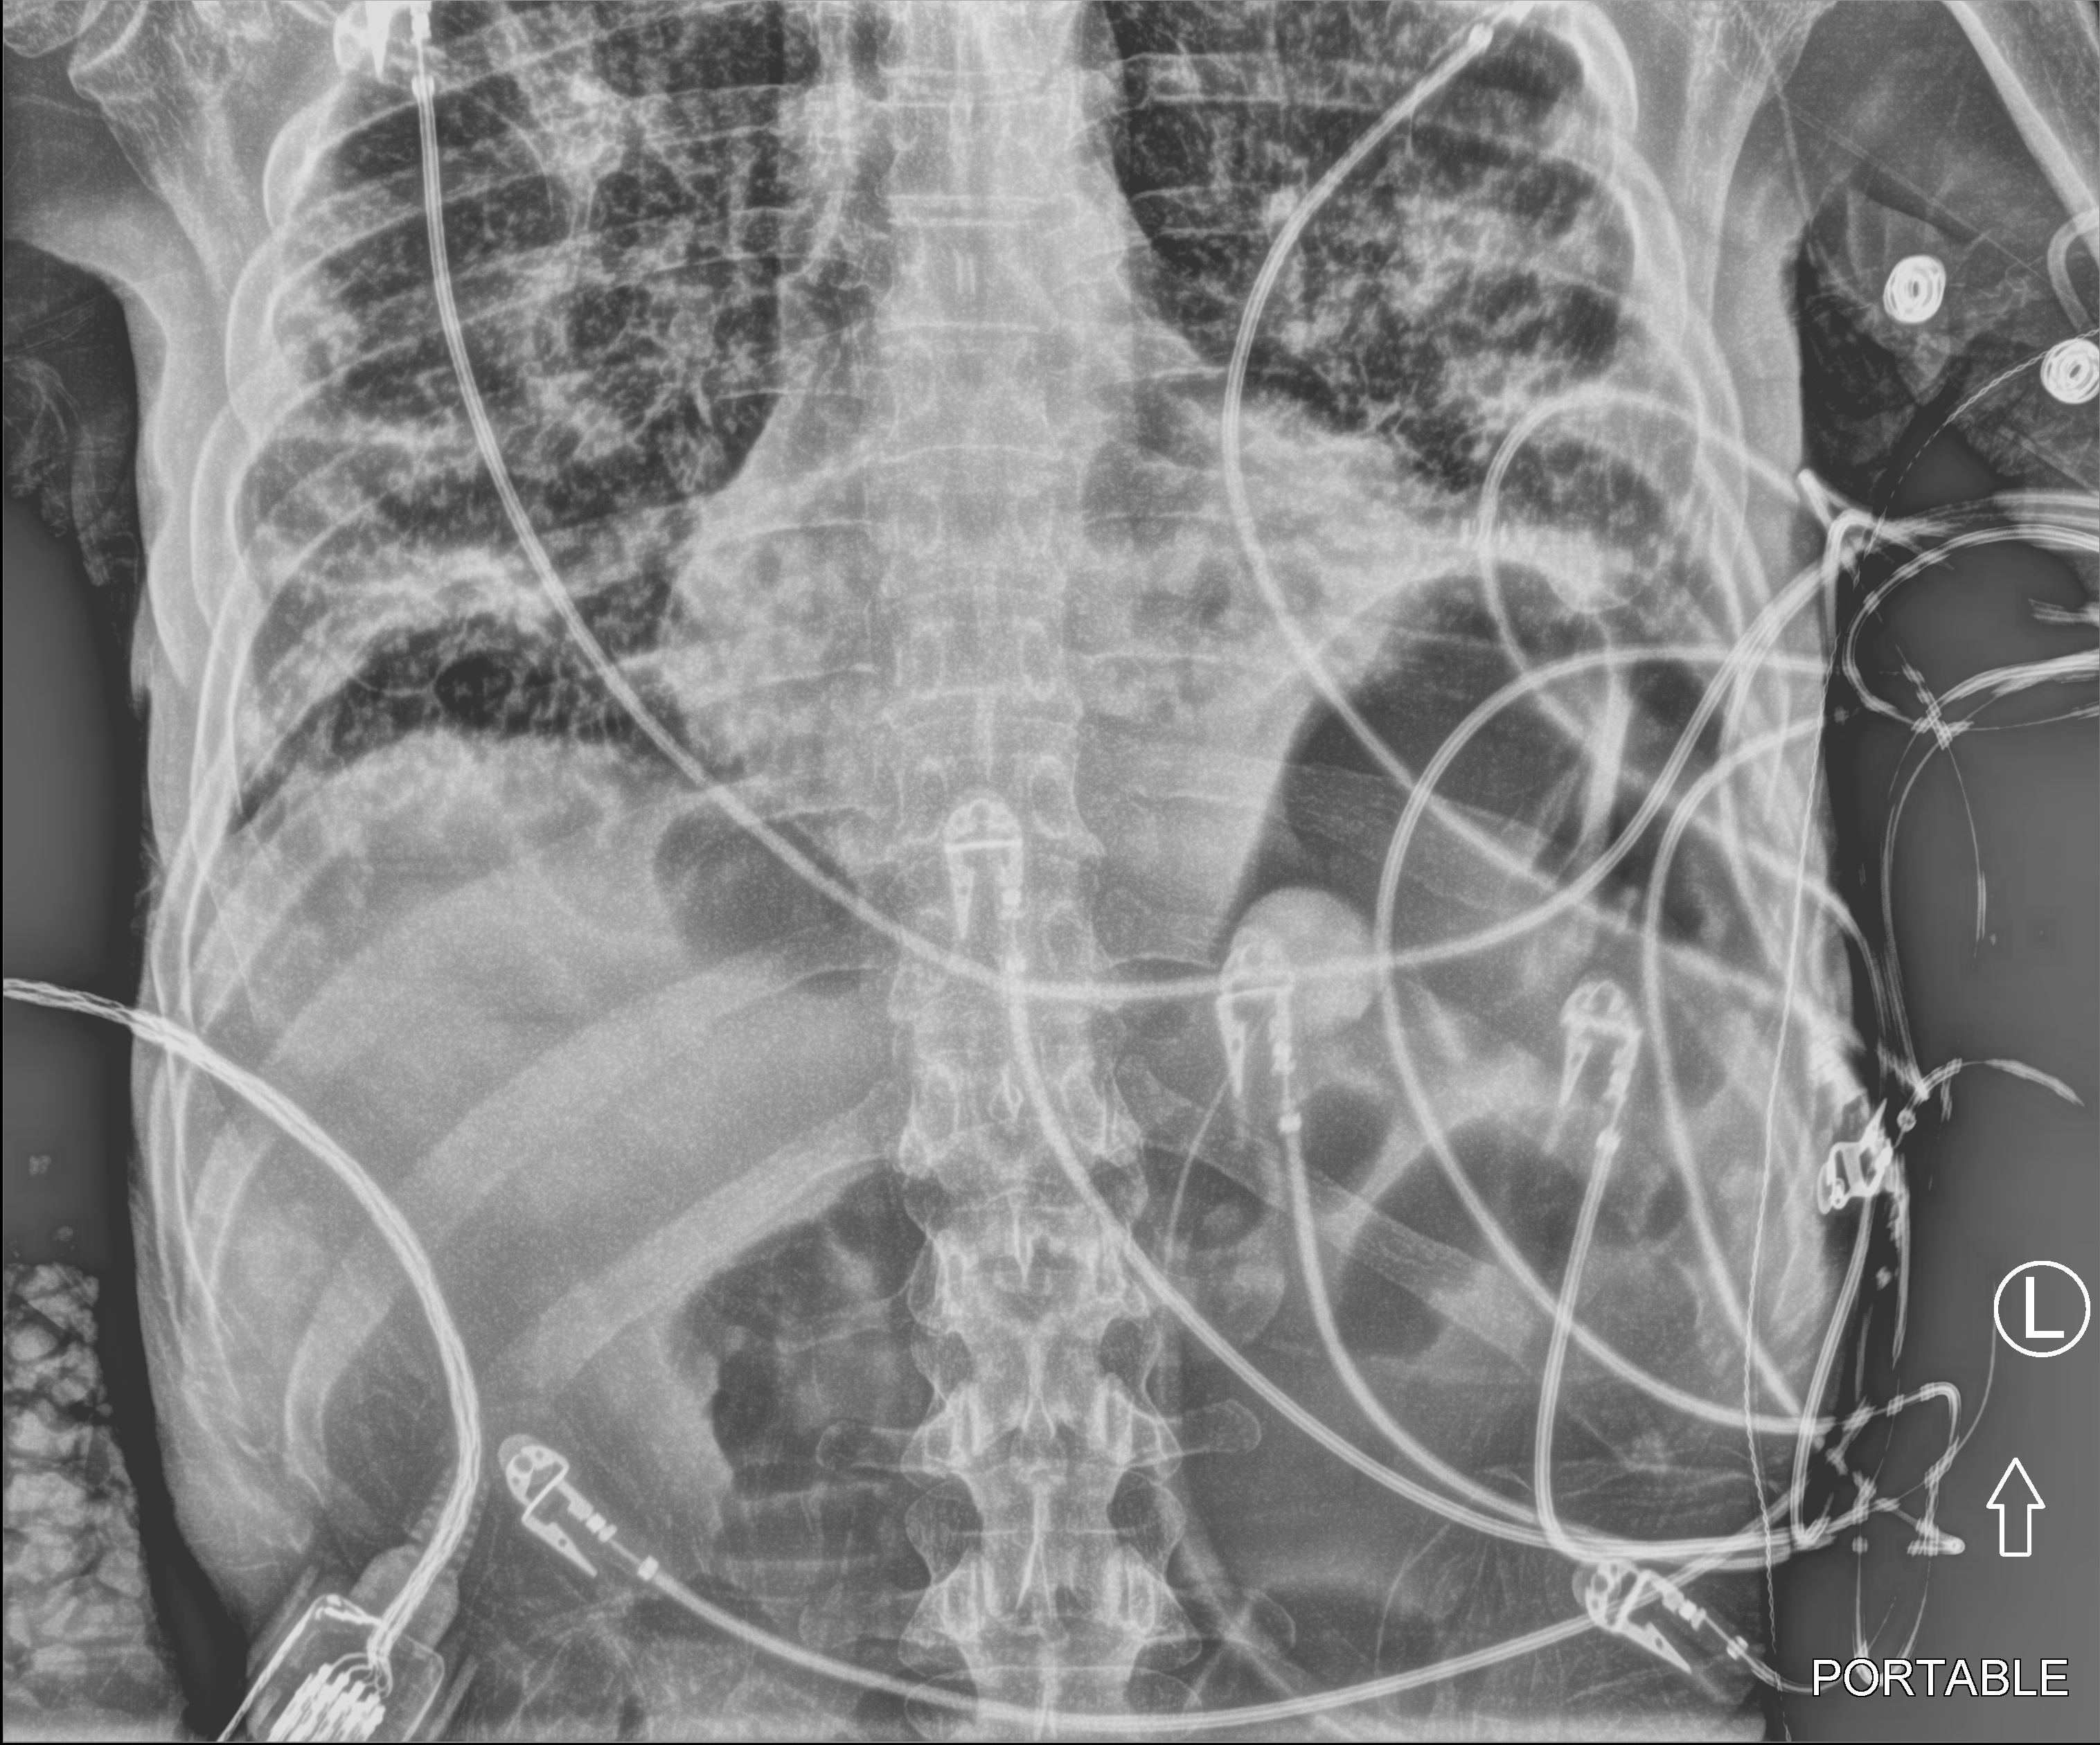
Bedside abdomen radiograph (computed radiography), anteroposterior (AP) projection. Patient hospitalised with COVID-19; male, aged 18–59 years.
Hospital-stay facts (about this admission, not read from this image; timing relative to this image not recorded):
- admitted to intensive care during this hospital stay: yes
- diabetes (admission record): yes
- mechanically ventilated during this hospital stay: yes